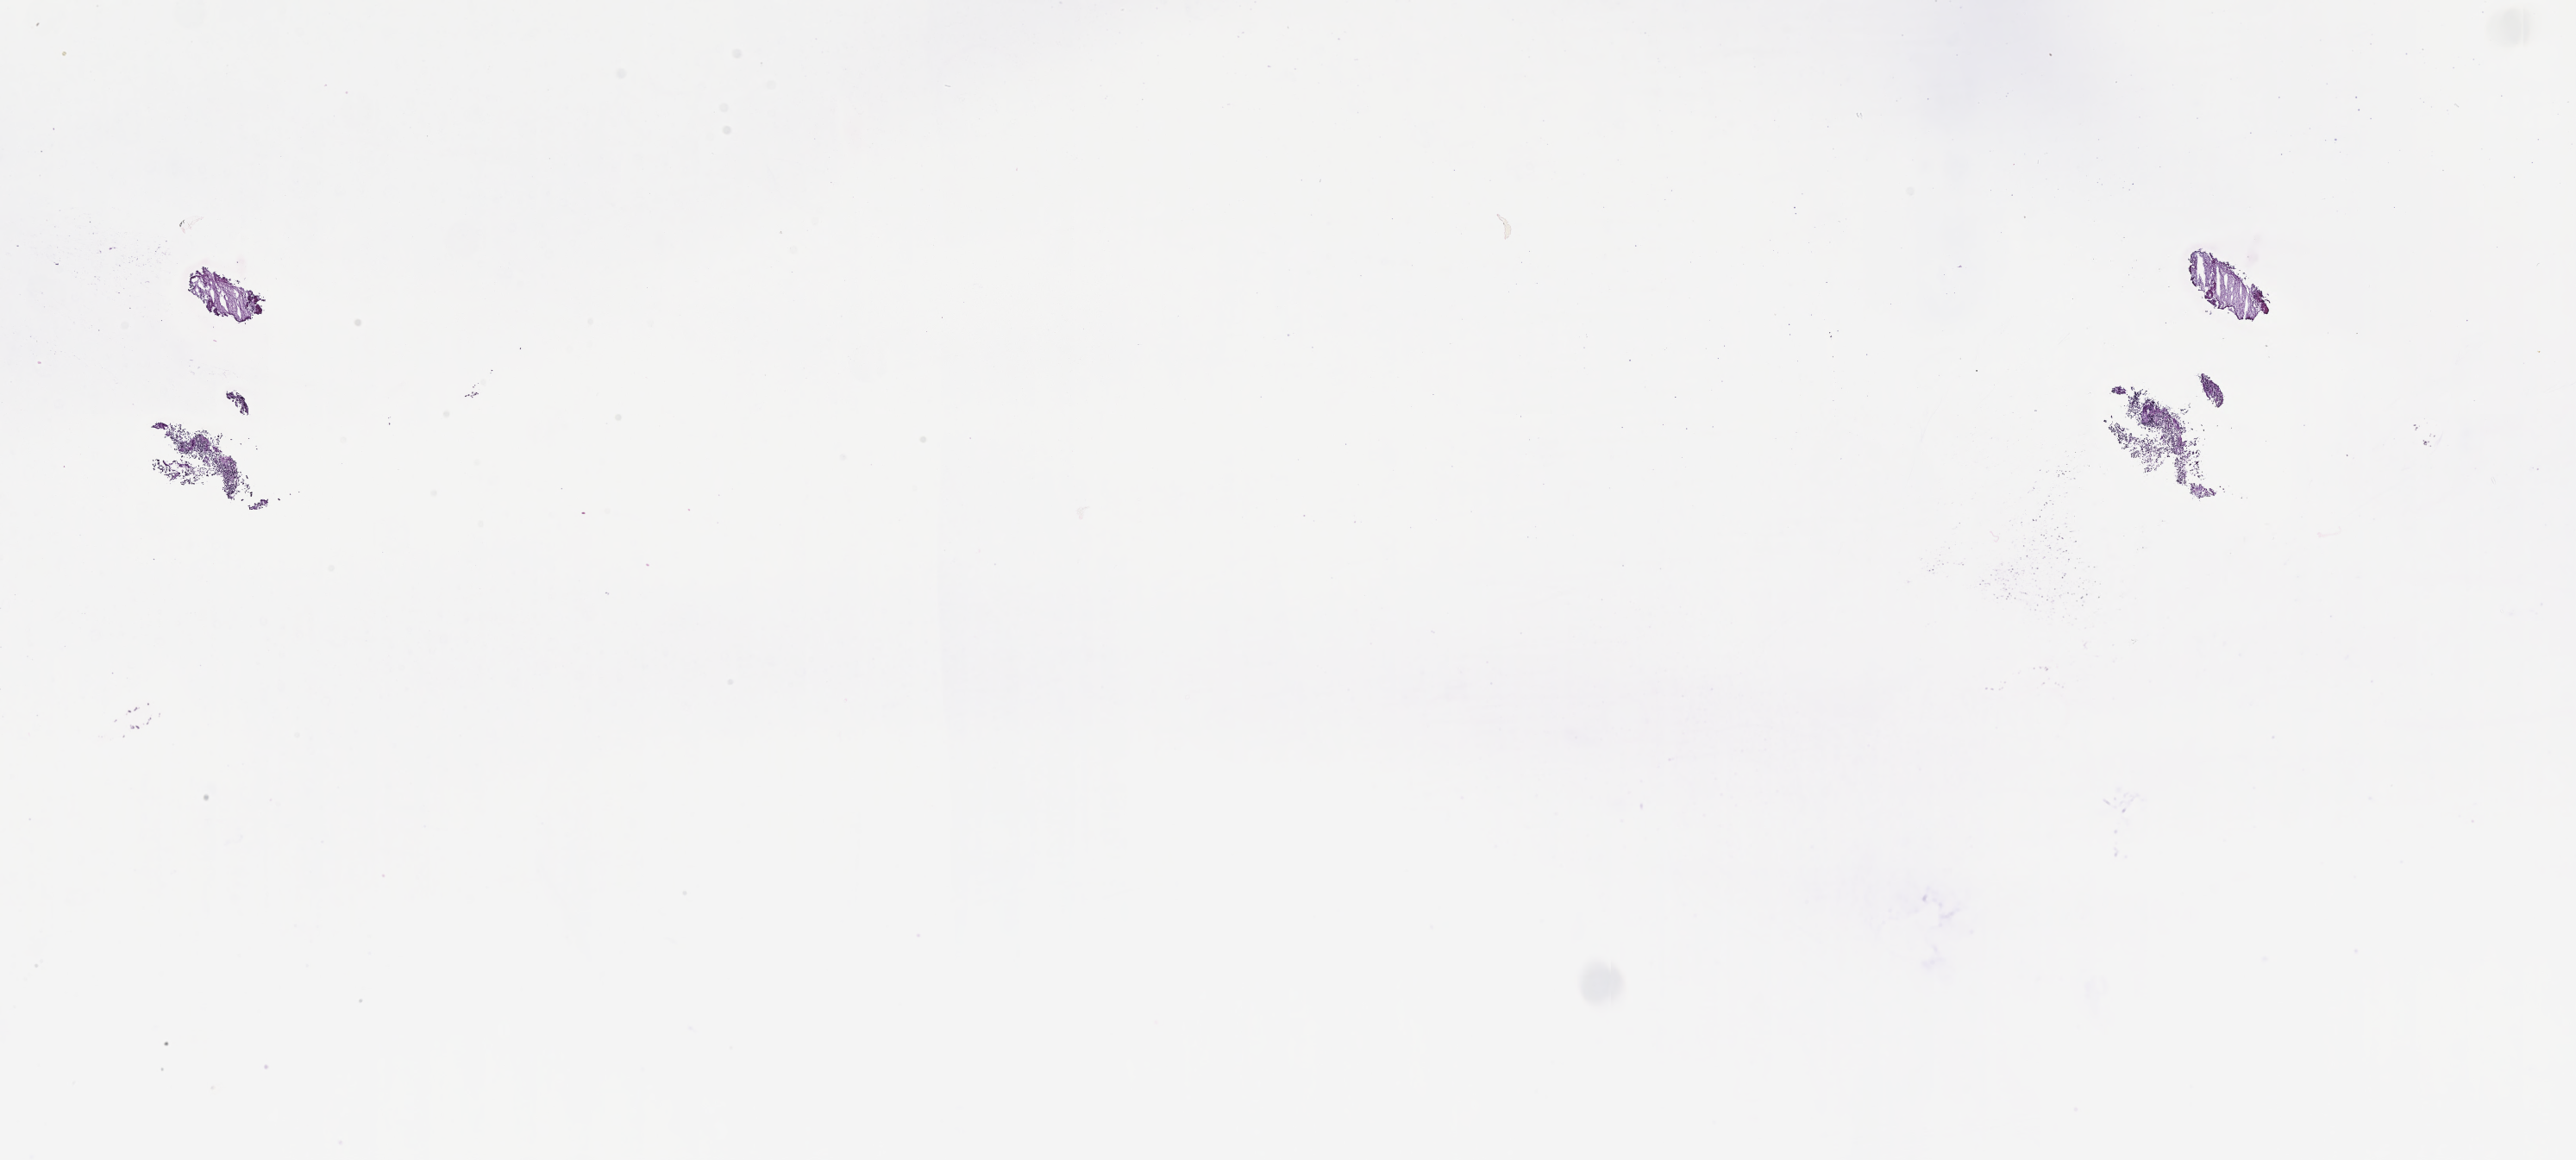
Haematoxylin and eosin whole-slide image of tumor tissue from the central nervous system — low-resolution overview of the scanned area, about 24.2 x 10.9 mm. Frozen section (OCT-embedded). Patient male; age 79 months (6 years 7 months).
• diagnosis: Medulloblastoma, NOS